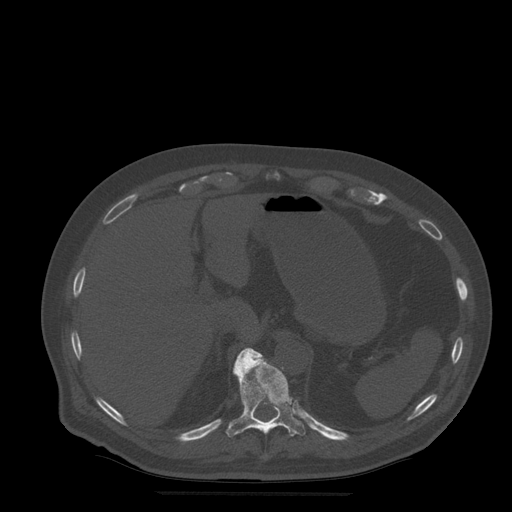
CT including the spine, one axial slice; bone window (W 1800 / L 400 HU); 512 × 512 image matrix. Patient age 72 years. From the clinical record (not read from this slice): primary cancer: prostate.
Outlined on this slice (semi-automatic segmentation, software-assisted and operator-edited):
- T11 vertebra: bounding box [x1, y1, x2, y2] px = [226, 348, 306, 438]